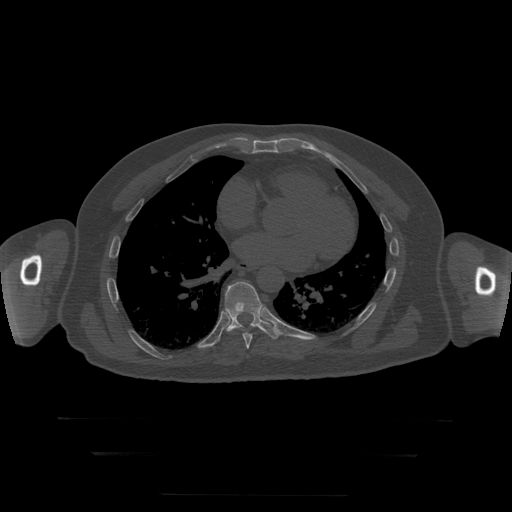
CT including the spine, one axial slice; slice 153 of 397 in the series (ordered by position); reconstruction kernel STANDARD; 120 kVp; bone window (W 1800 / L 400 HU); 1.25 mm slice thickness; 512 × 512 image matrix, field of view 510 × 510 mm. Patient age 73 years. Case-level facts recorded for this patient, not image findings: primary cancer: prostate.
Outlined on this slice (semi-automatic segmentation, software-assisted and operator-edited):
- T8 vertebra: bounding box <226,311,253,350> (left, top, right, bottom; pixels)
- T9 vertebra: <225,282,280,340>